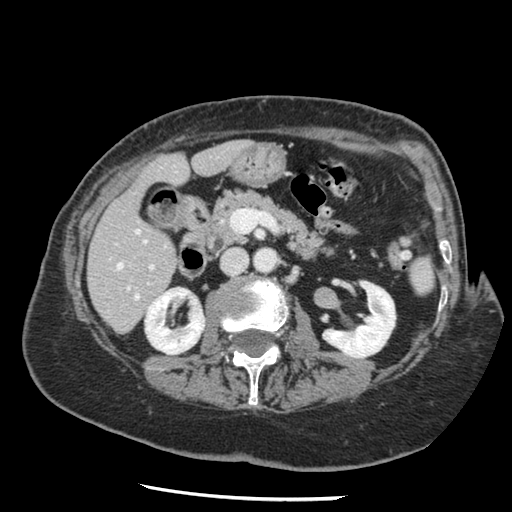
Contrast-enhanced abdominal CT, one axial slice. 120 kVp. Intravenous contrast given. Soft-tissue window (W 400 / L 40 HU). 512 × 512 image matrix, field of view 330 × 330 mm. Female patient, age 85 years. From the clinical record (not read from this slice): diagnosis: colorectal cancer liver metastases, imaged before liver resection; multiple liver metastases: no; largest metastasis: 0.9 cm; disease in both lobes: no.
Structures marked on this image (expert manual segmentation):
- hepatic veins: box from (x=117, y=230) to (x=140, y=299) px
- liver: (x=89, y=141)–(x=247, y=333)
- planned liver remnant (the part of the liver to remain after resection): (x=89, y=141)–(x=247, y=332)
- portal vein (with intrahepatic branches): (x=151, y=266)–(x=153, y=268)